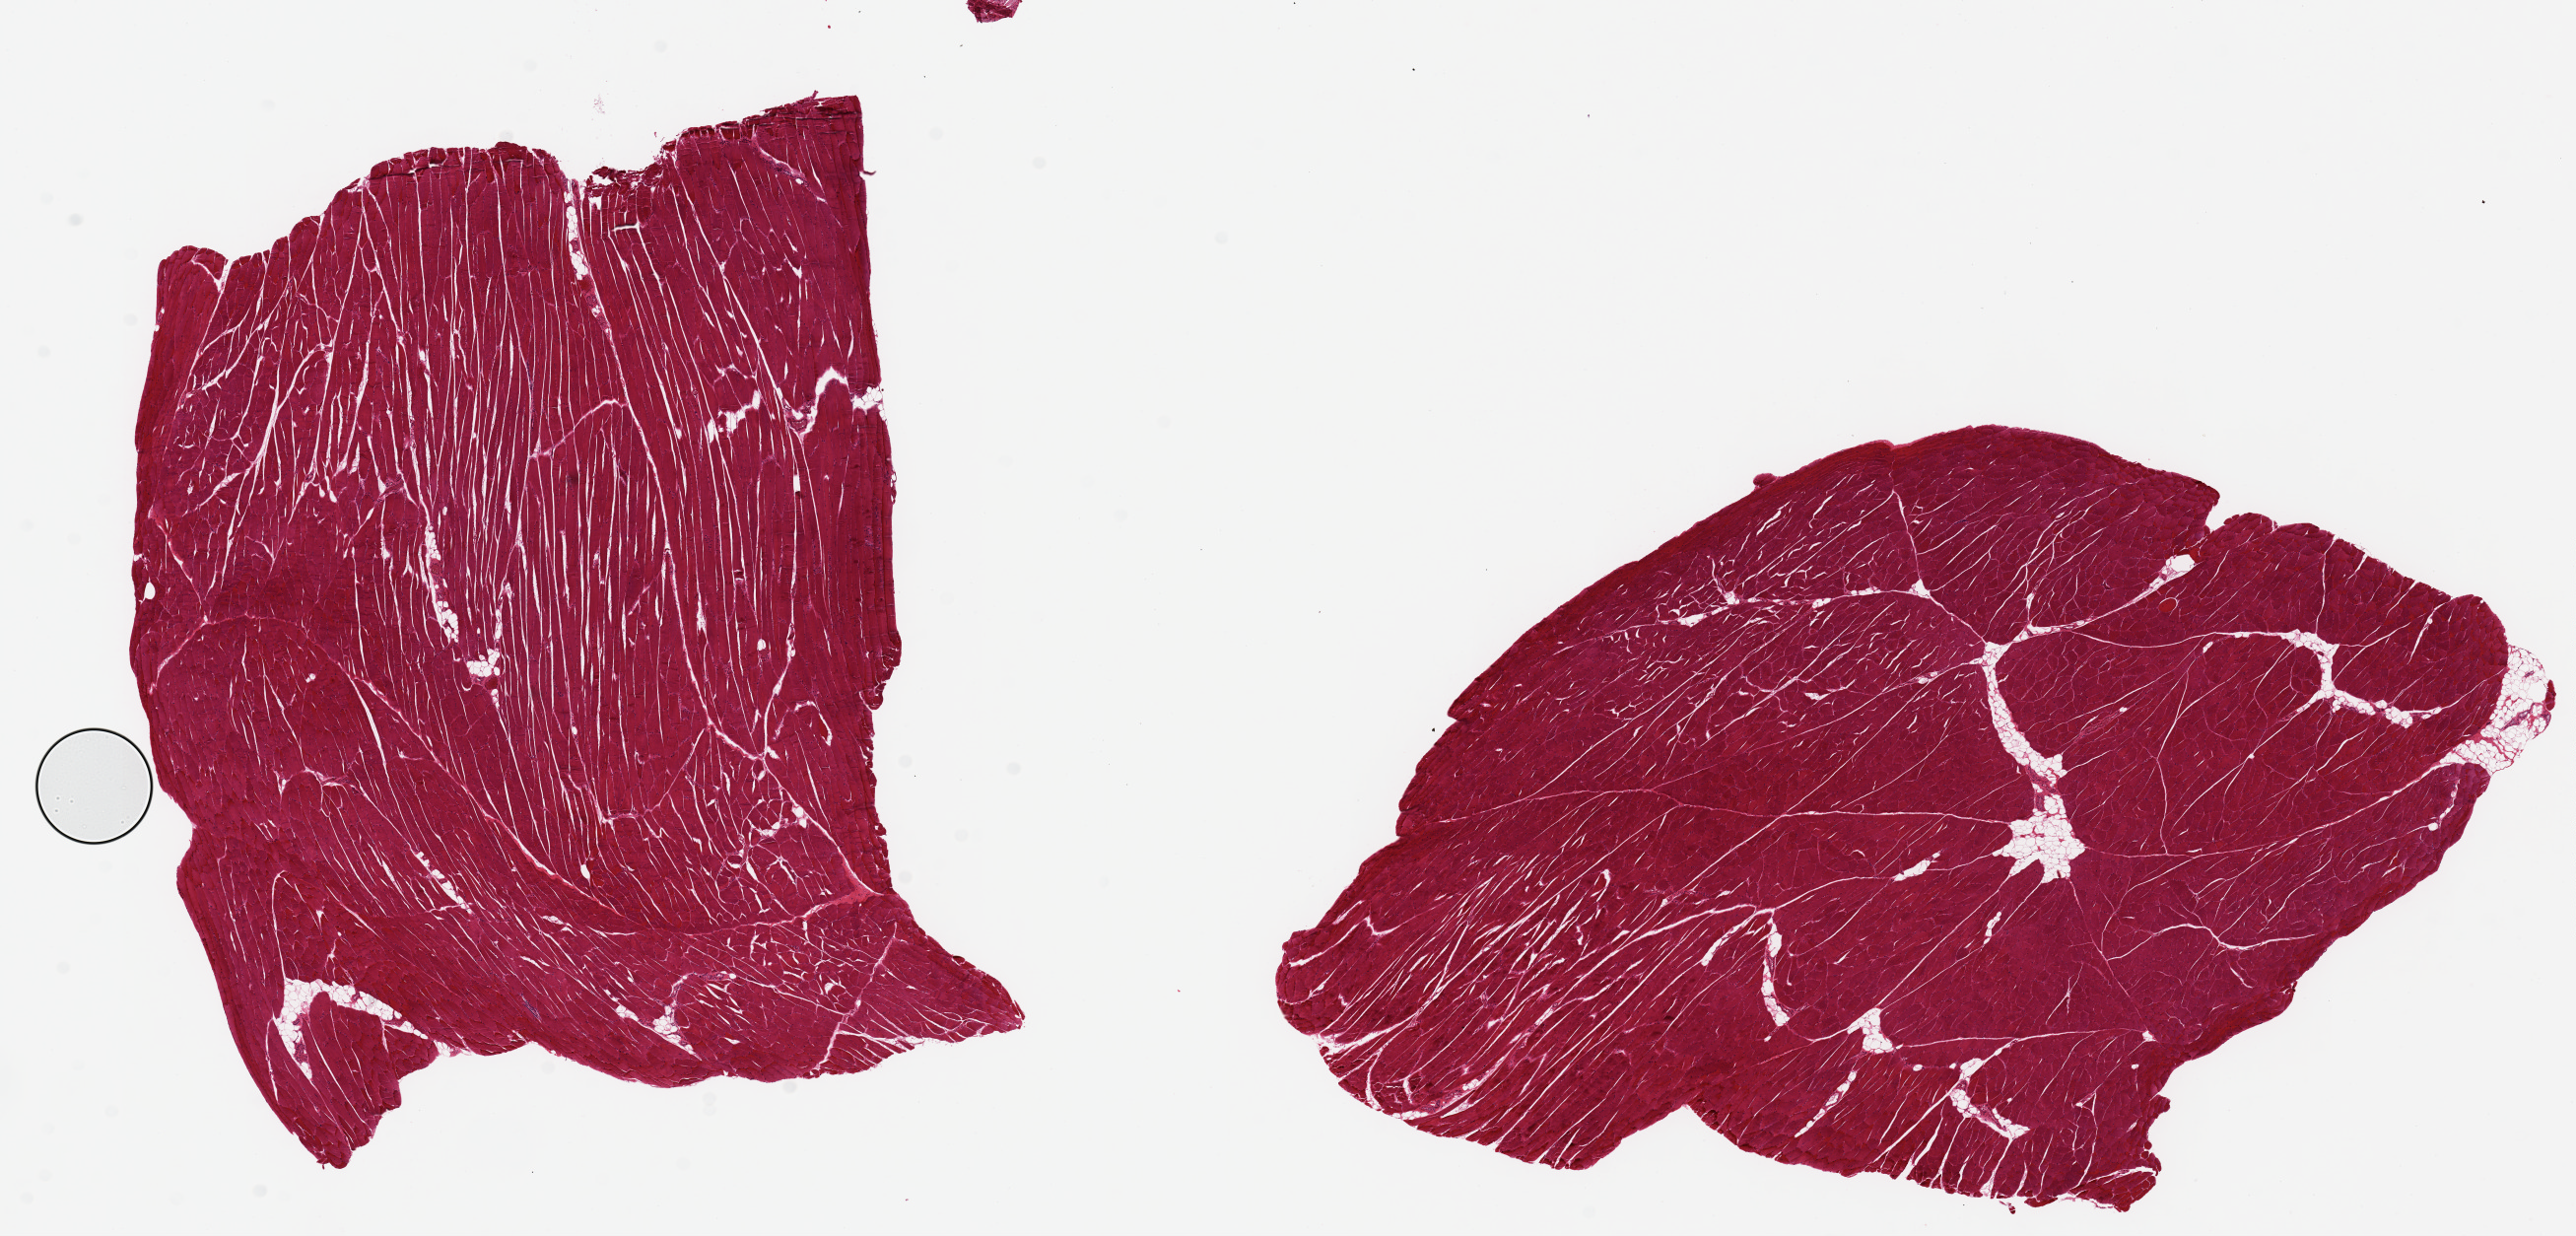
Hematoxylin and eosin (H&E) whole-slide image, brightfield — a low-resolution overview of the entire scanned area, about 20.7 x 9.9 mm, PAXgene-fixed paraffin-embedded (PFPE) section, section of skeletal muscle (target tissue), tissue donor sample.
Review note (as recorded): 2 pieces ~7x7mm, < 5% interstitial fat.